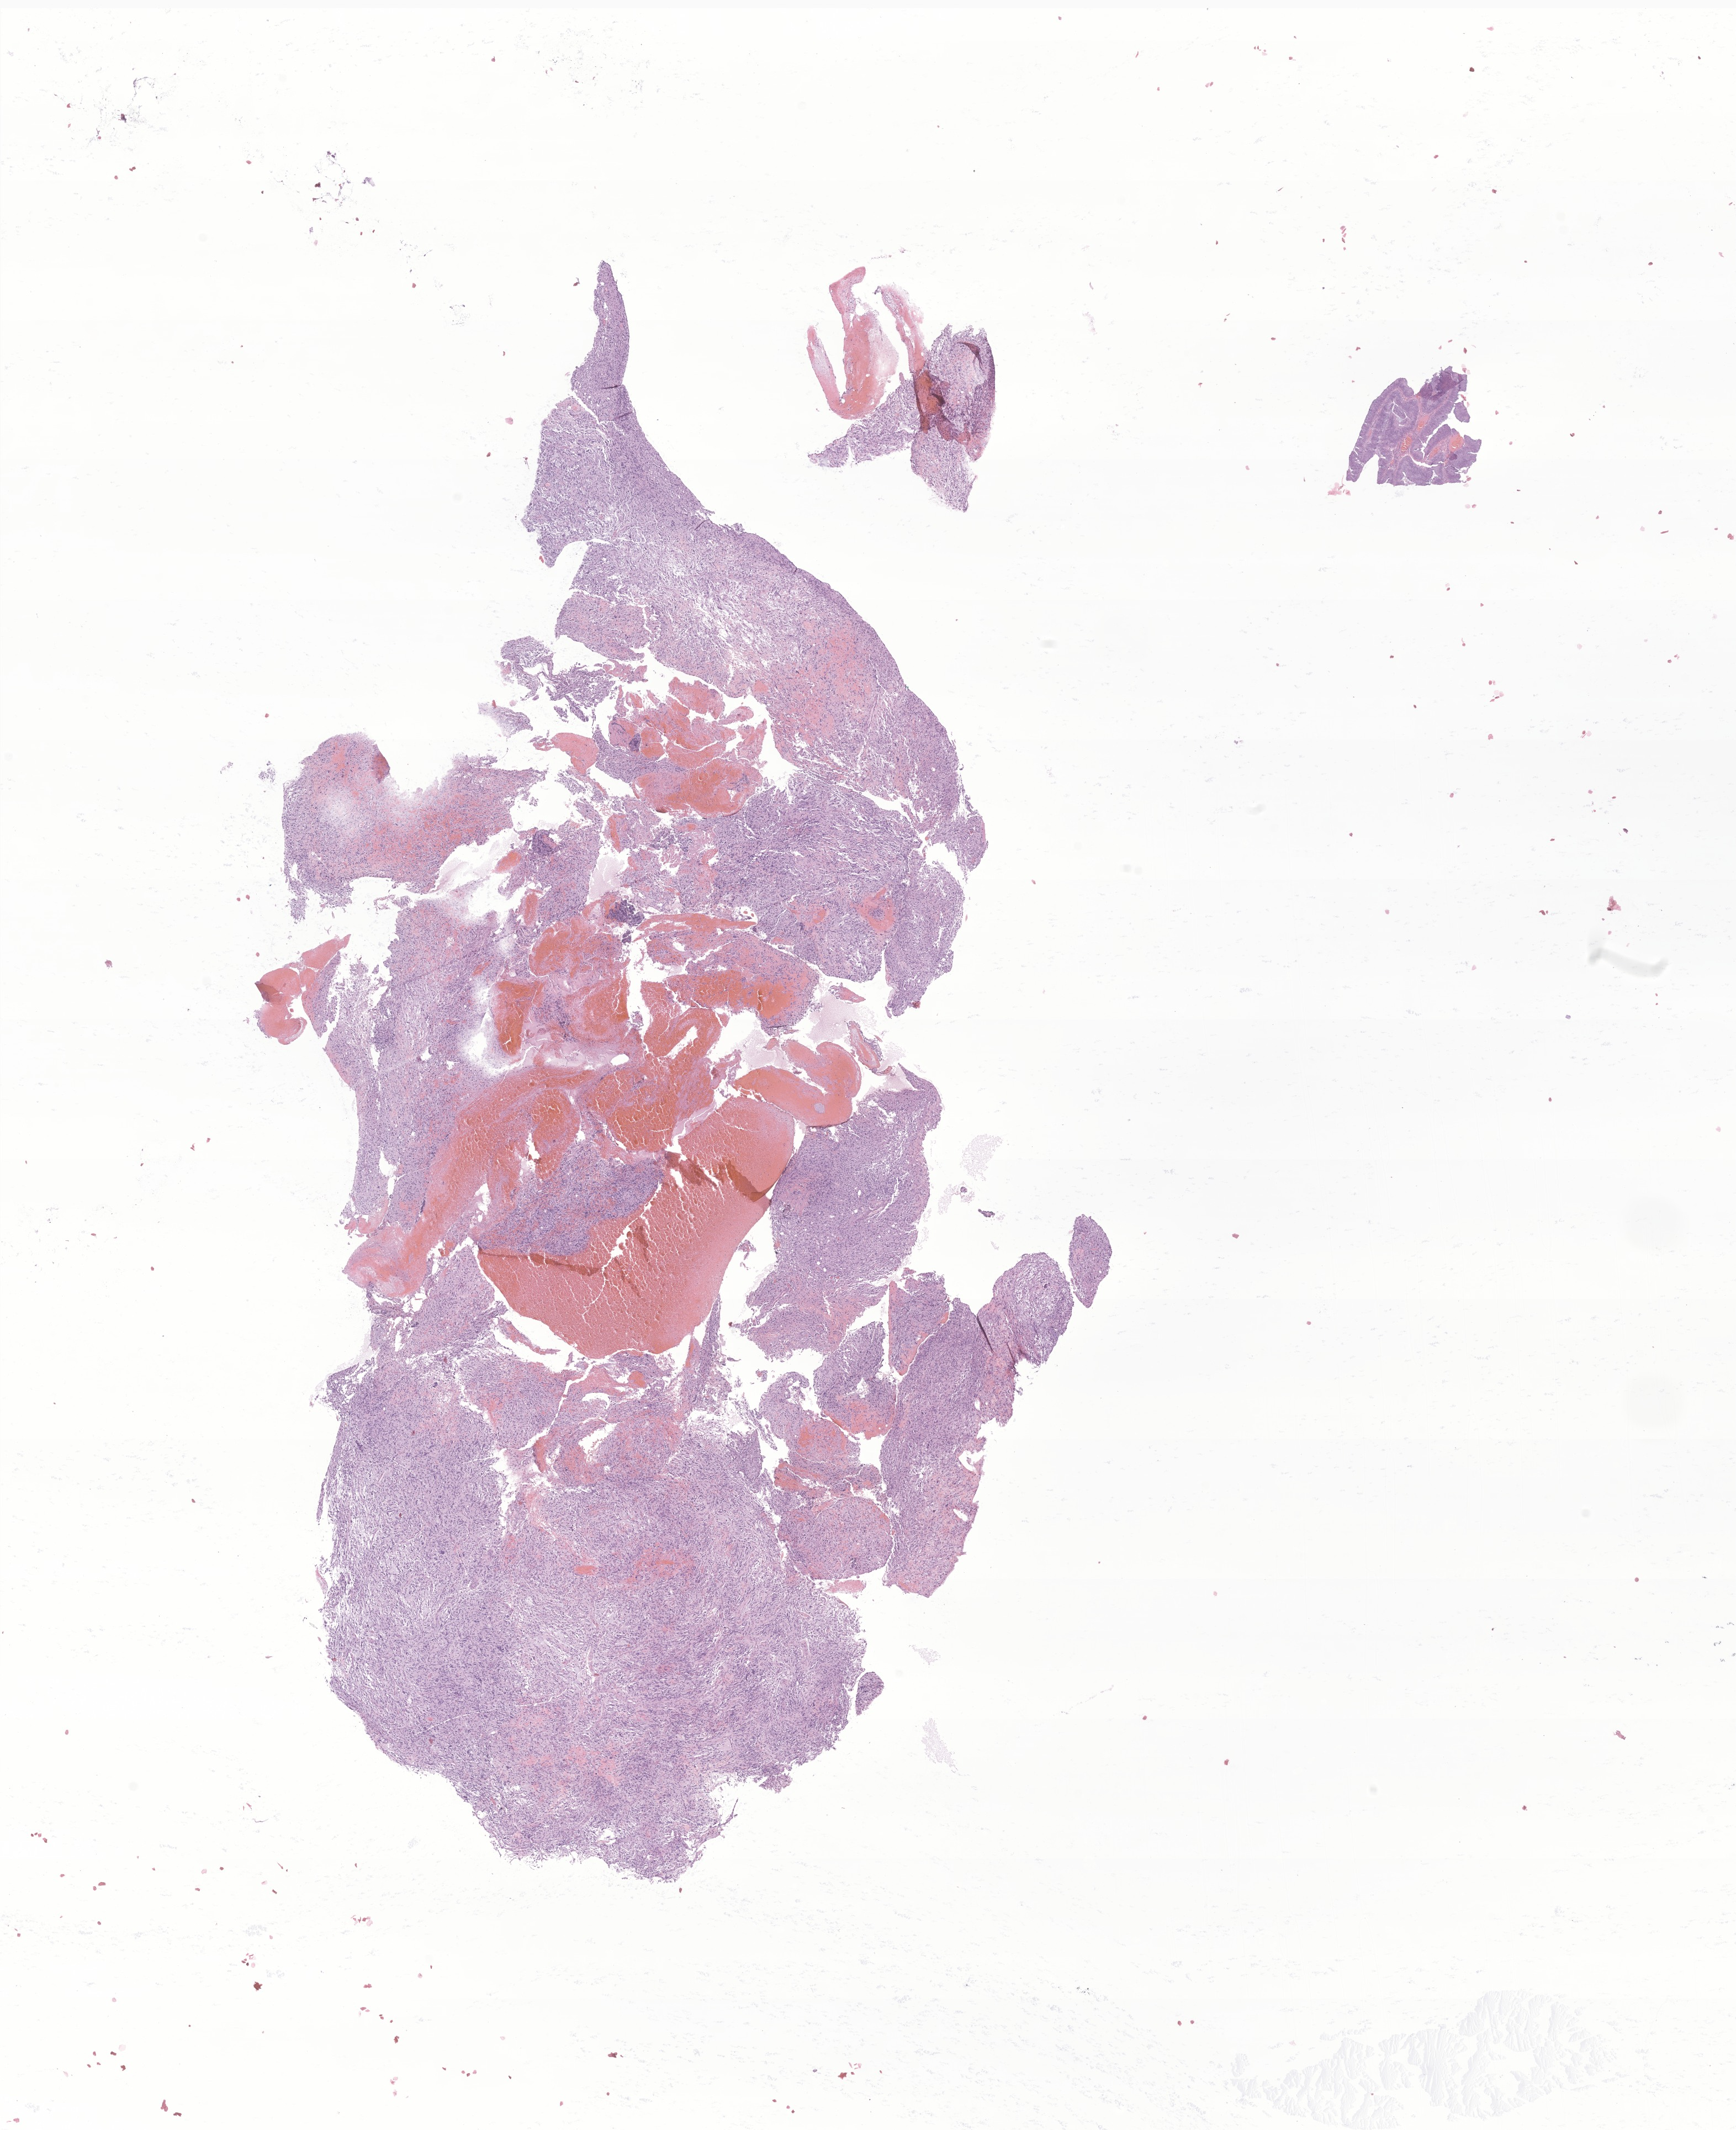
Digitized H&E-stained section of tumor tissue from the brain, a low-resolution overview of the entire scanned area, about 13.3 x 16.3 mm. FFPE section. Patient male; age 219 months (18 years 3 months).
• diagnosis: Neoplasm, uncertain whether benign or malignant